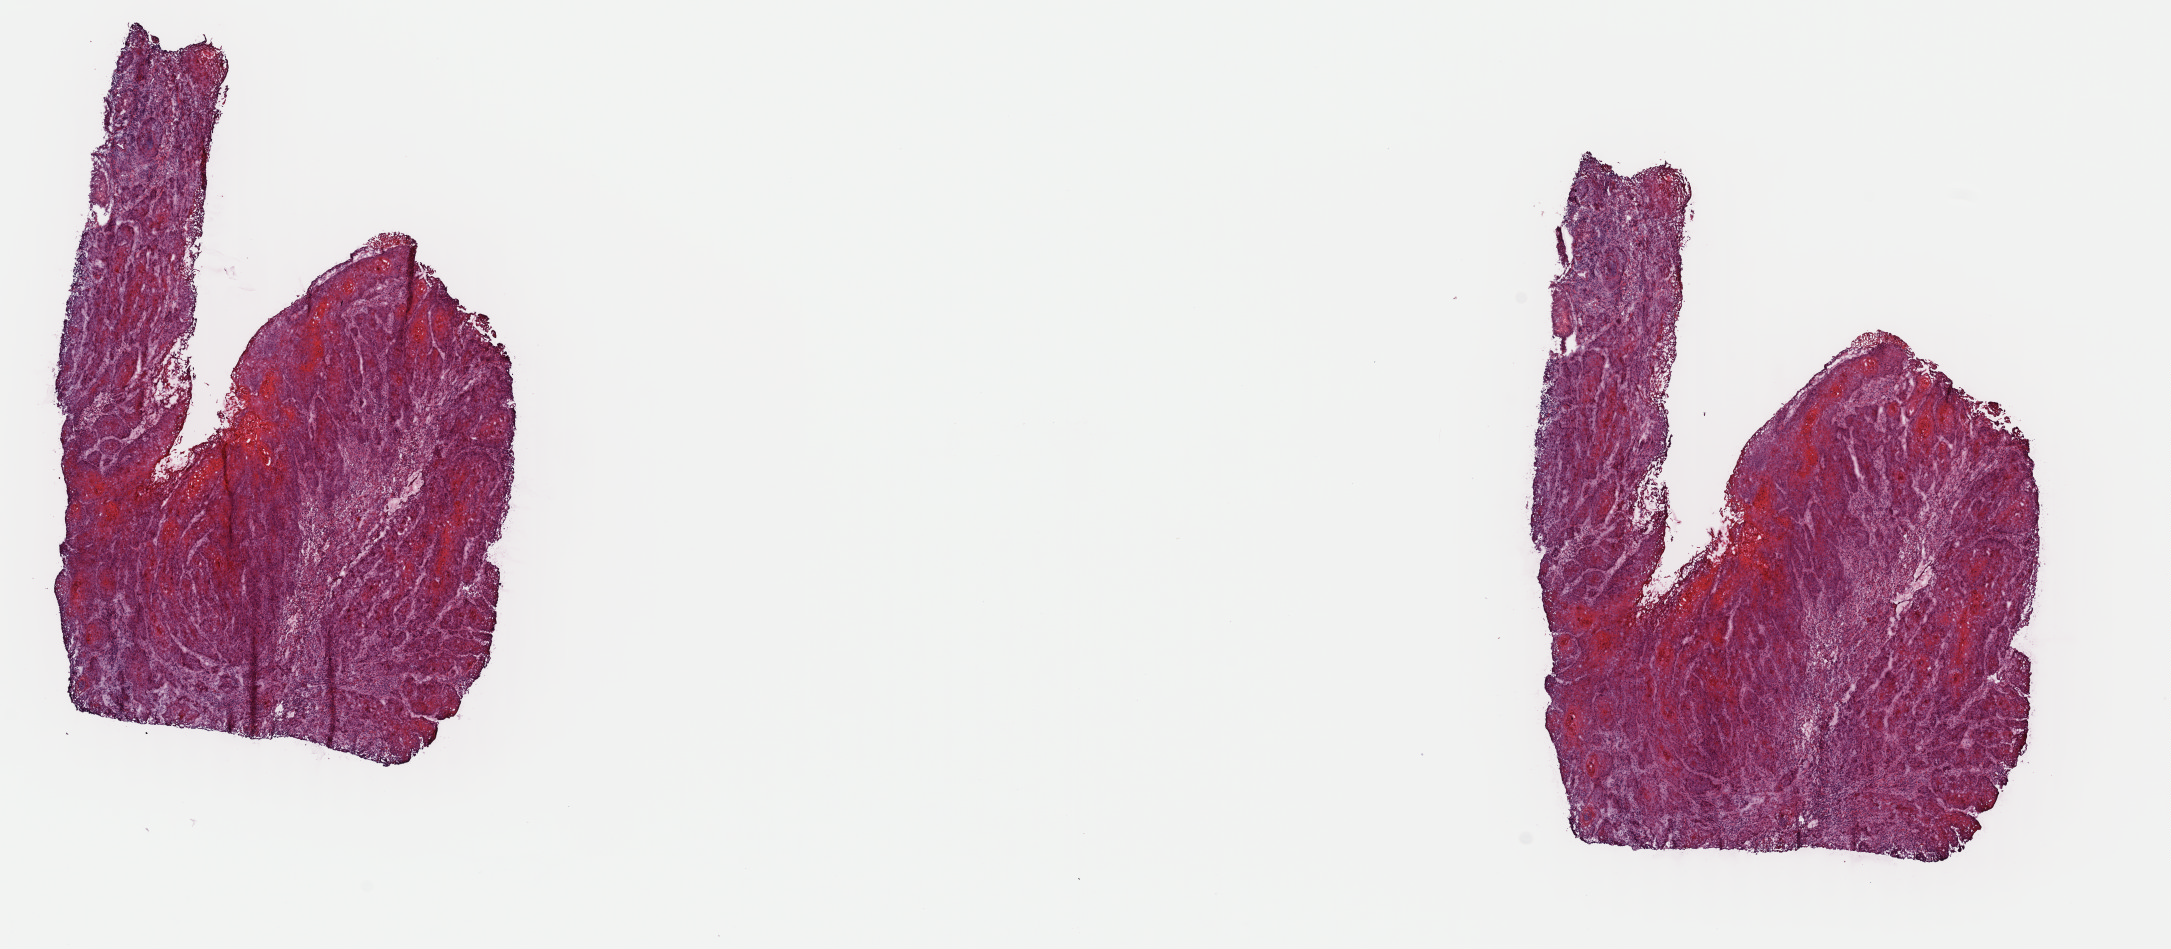
Digitized H&E-stained tissue section (whole slide) — a low-resolution overview of the entire scanned area, about 17.1 x 7.5 mm (acquisition: 40x scan). Frozen section from the top of the tissue portion. Sample: primary tumour, head and neck. Patient: male, age at initial diagnosis 52 years. Histologic grade: G2 (moderately differentiated). Slide review estimates, as recorded: tumour cells 100%, tumour nuclei 80%, normal cells 0%, stromal cells 0%, necrosis 0%. Infiltration values recorded for this section: lymphocyte infiltration 3%, monocyte infiltration 0%, neutrophil infiltration 0%.
AJCC pathologic stage: IVA (7th edition). Histologic diagnosis: Squamous cell carcinoma, NOS (floor of mouth, NOS). TNM: T4a N2c M0. Lymph nodes positive (case pathology): 4 of 58 examined. Laterality: left.